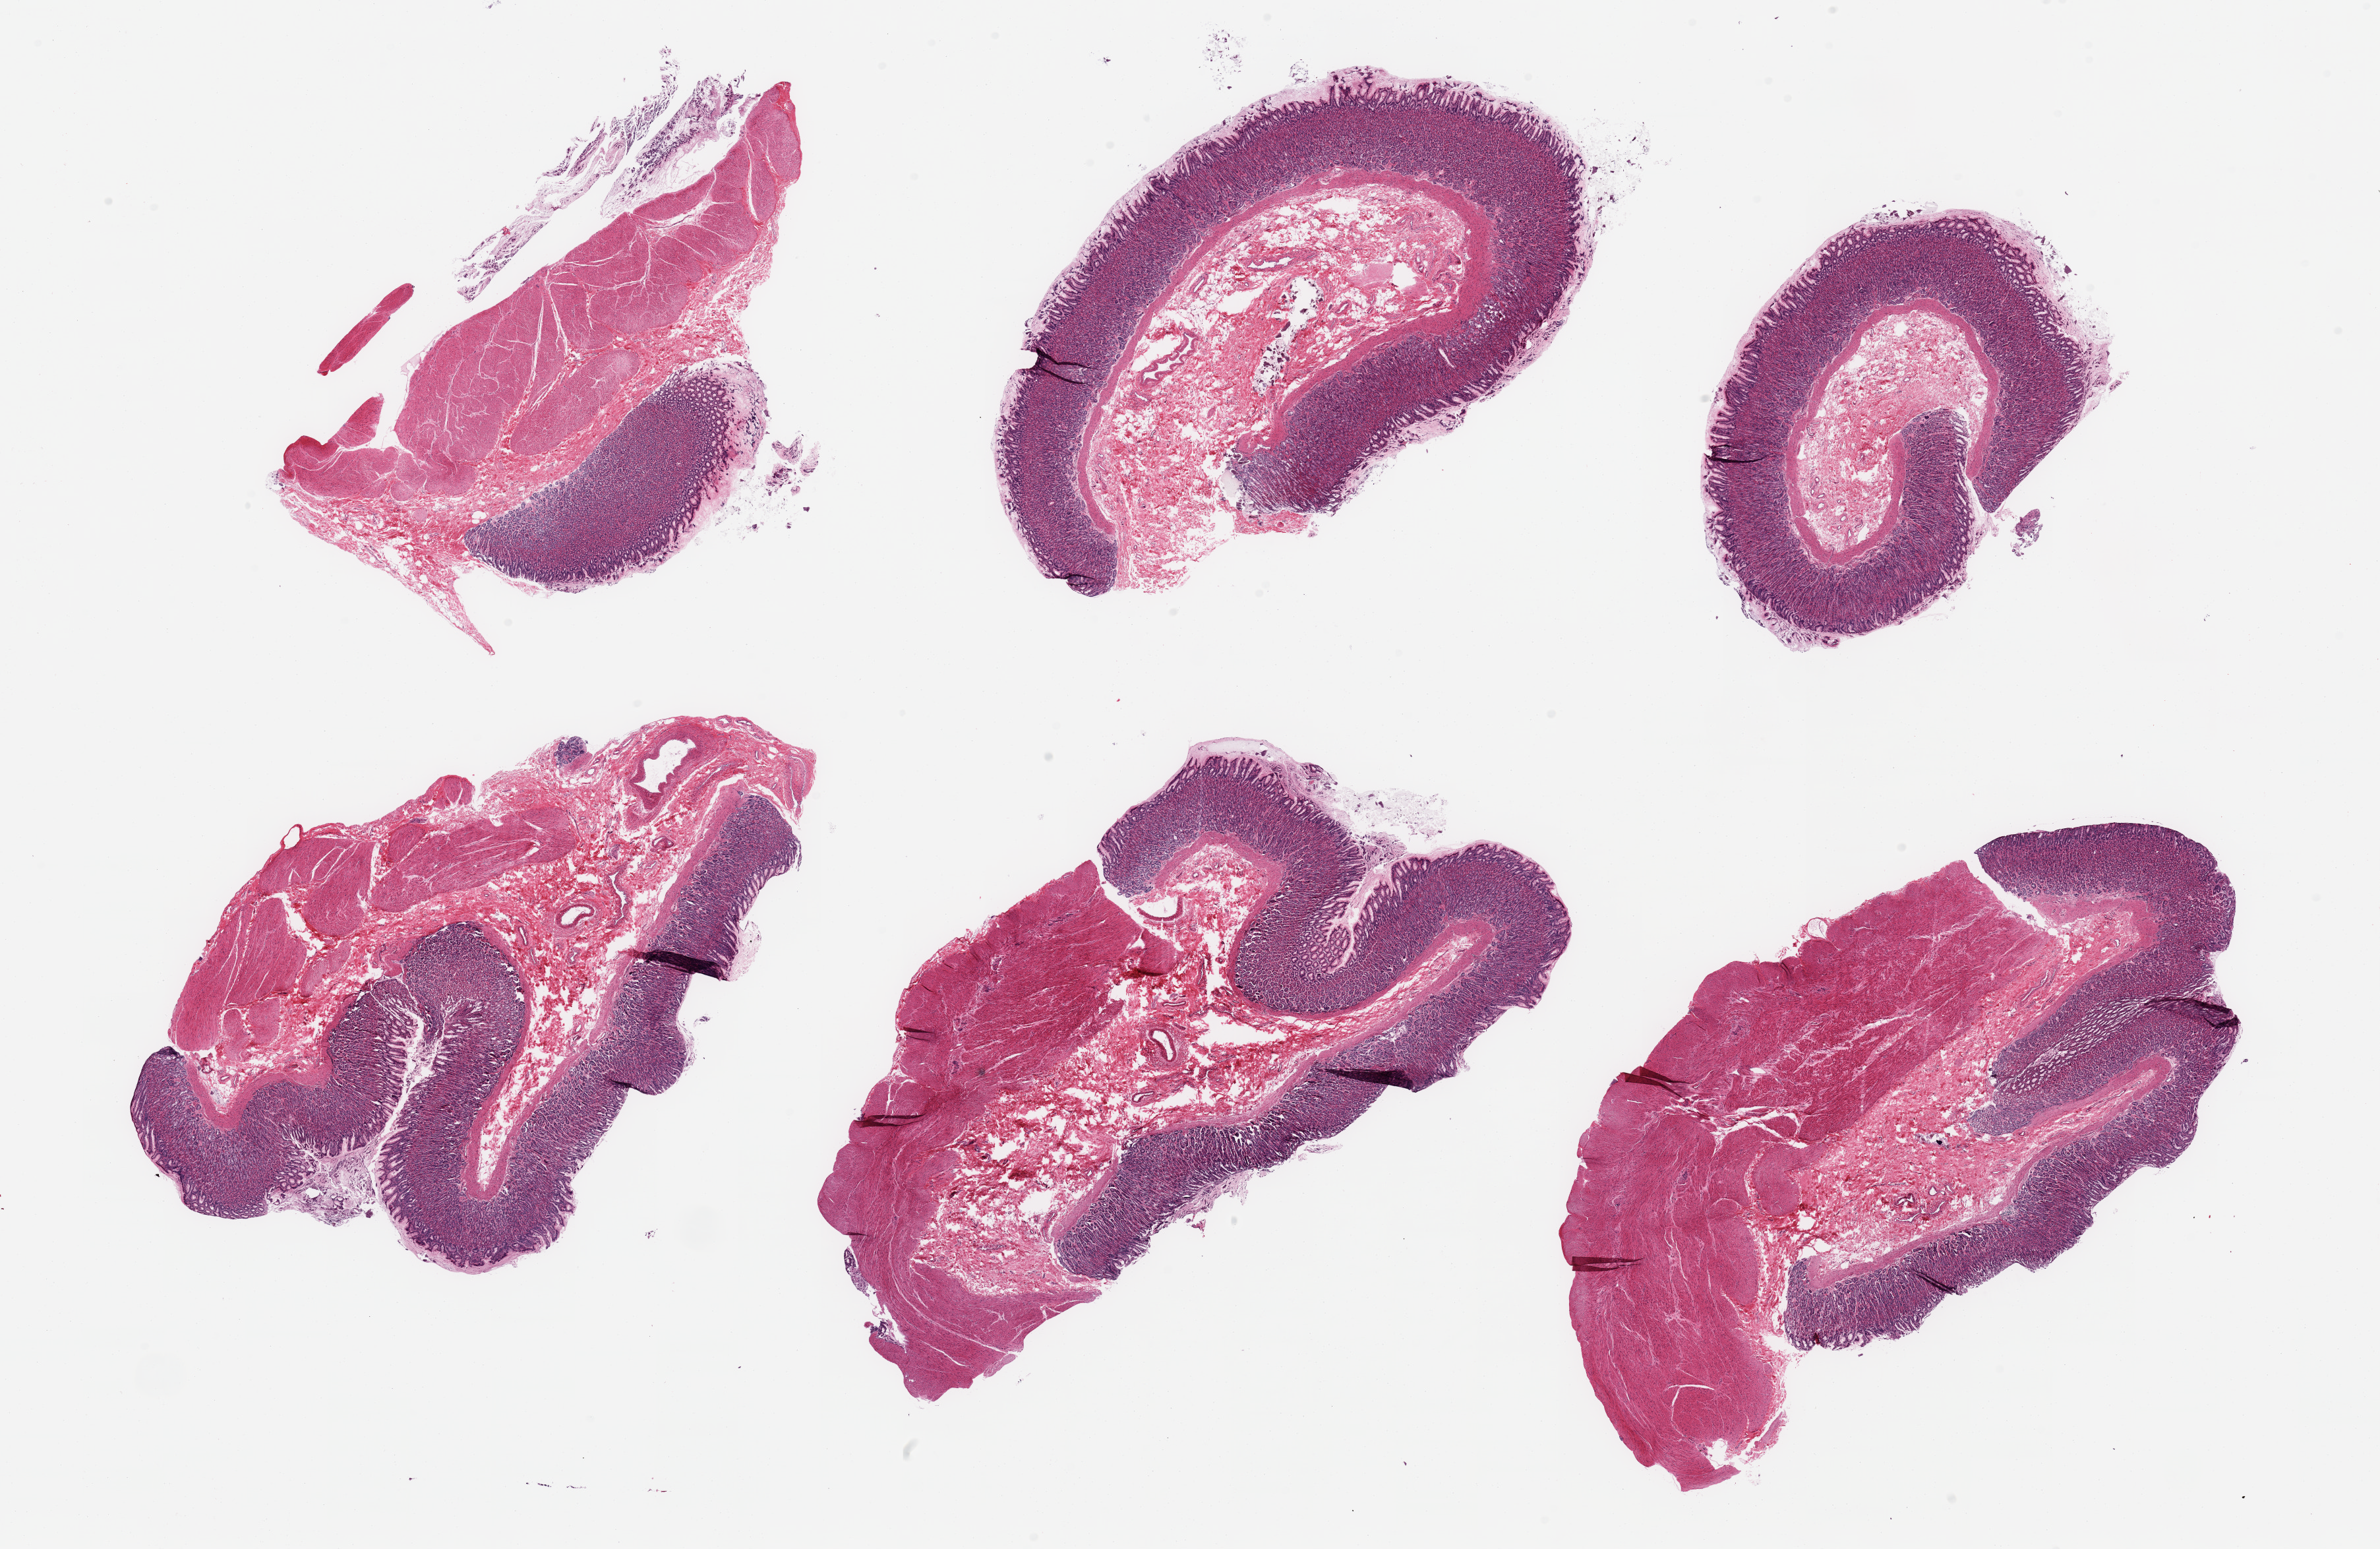
Hematoxylin and eosin (H&E) whole-slide image — whole scanned area (about 28.5 x 18.6 mm, slide scanned at 20x) shown as a low-resolution overview; PAXgene-fixed paraffin-embedded (PFPE) section; section of stomach (target tissue); donor tissue sample. Donor: female.
Pathologist's review note for this sample: 6 pieces, target mucosa well-preserved, ~25-30% thickness, excellent specimen.